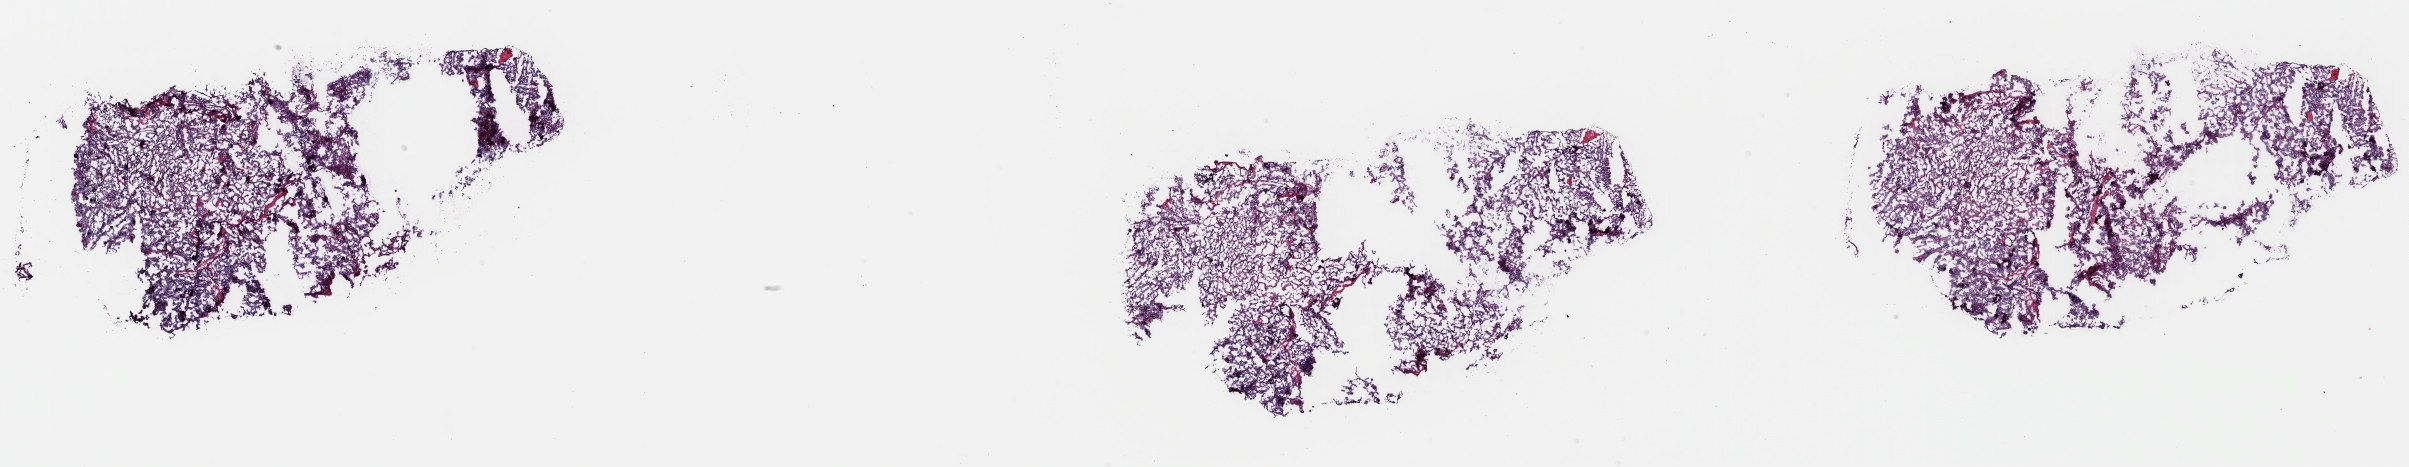
Digitized Hematoxylin and eosin (H&E) stained tissue section (whole slide) — low-resolution overview of the scanned area, about 38.1 x 7.4 mm; frozen section from the top of the tissue portion; thyroid, primary tumour sample. Female, age 22 years at initial diagnosis. Composition of this section per pathologist review: tumour cells 80%, tumour nuclei 80%, normal cells 0%, stromal cells 20%, necrosis 0%. Inflammatory infiltration, as recorded: lymphocyte infiltration 2%, monocyte infiltration 0%, neutrophil infiltration 0%.
AJCC pathologic stage: I. Lymph nodes positive (case pathology): 13 of 40 examined. Laterality: midline. TNM: T1a N1 M0. Histologic diagnosis: Papillary adenocarcinoma, NOS (thyroid gland).